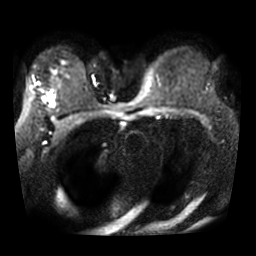
Breast MRI, one axial slice. Diffusion-weighted series; image 2 of 4 stored at this slice position (different b-values; order by instance number). 3 T. 256 × 256 image matrix. Female patient.
Outlined on this slice (expert manual segmentation):
- tumour on diffusion-weighted imaging: bounding box (x1, y1, x2, y2) in pixels: (50, 94, 54, 100)